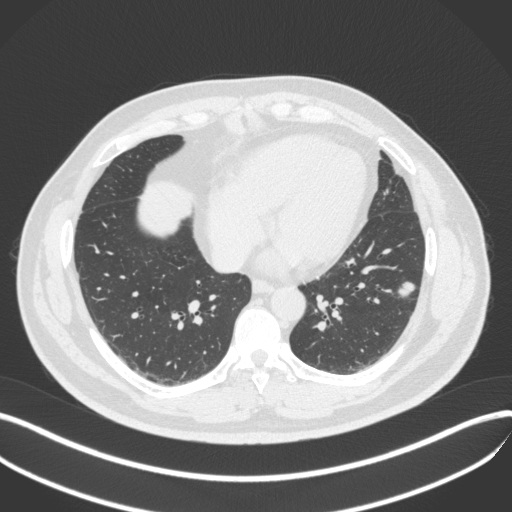
Chest CT, one axial slice. Slice 153 of 420 in the series (ordered by position). 120 kVp. Lung window (W 1500 / L -600 HU). 512 × 512 image matrix. Male patient, age 39 years. Case-level facts recorded for this patient, not image findings: clinical TNM (as recorded): T2a N0 M0.
Outlined on this slice (bounding box drawn by a radiologist):
- lung tumour (recorded histology: adenocarcinoma): bounding box (x1, y1, x2, y2) in pixels: (396, 275, 418, 303)